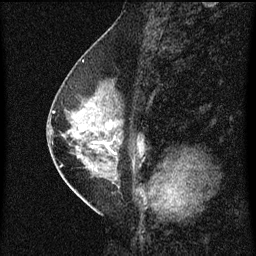
Breast MRI (dynamic contrast-enhanced), one sagittal slice. Slice 30 of 60 in the series (ordered by position). Dynamic contrast-enhanced series, image 2 of 3 at this slice position (ordered by acquisition). 1.5 T. TE 4.2 ms, TR 8 ms. 2 mm slice thickness. 256 × 256 image matrix, field of view 180 × 180 mm. Female patient, age 47 years.
Outlined on this slice (semi-automatic segmentation, software-assisted and operator-edited):
- analysis volume of interest (the breast-tissue region the enhancement analysis was run in; not a lesion): bounding box <54,80,145,187> (left, top, right, bottom; pixels)
- tumour enhancement mask (voxels above the 70 % enhancement threshold inside the analysis volume of interest): <140,148,142,151>